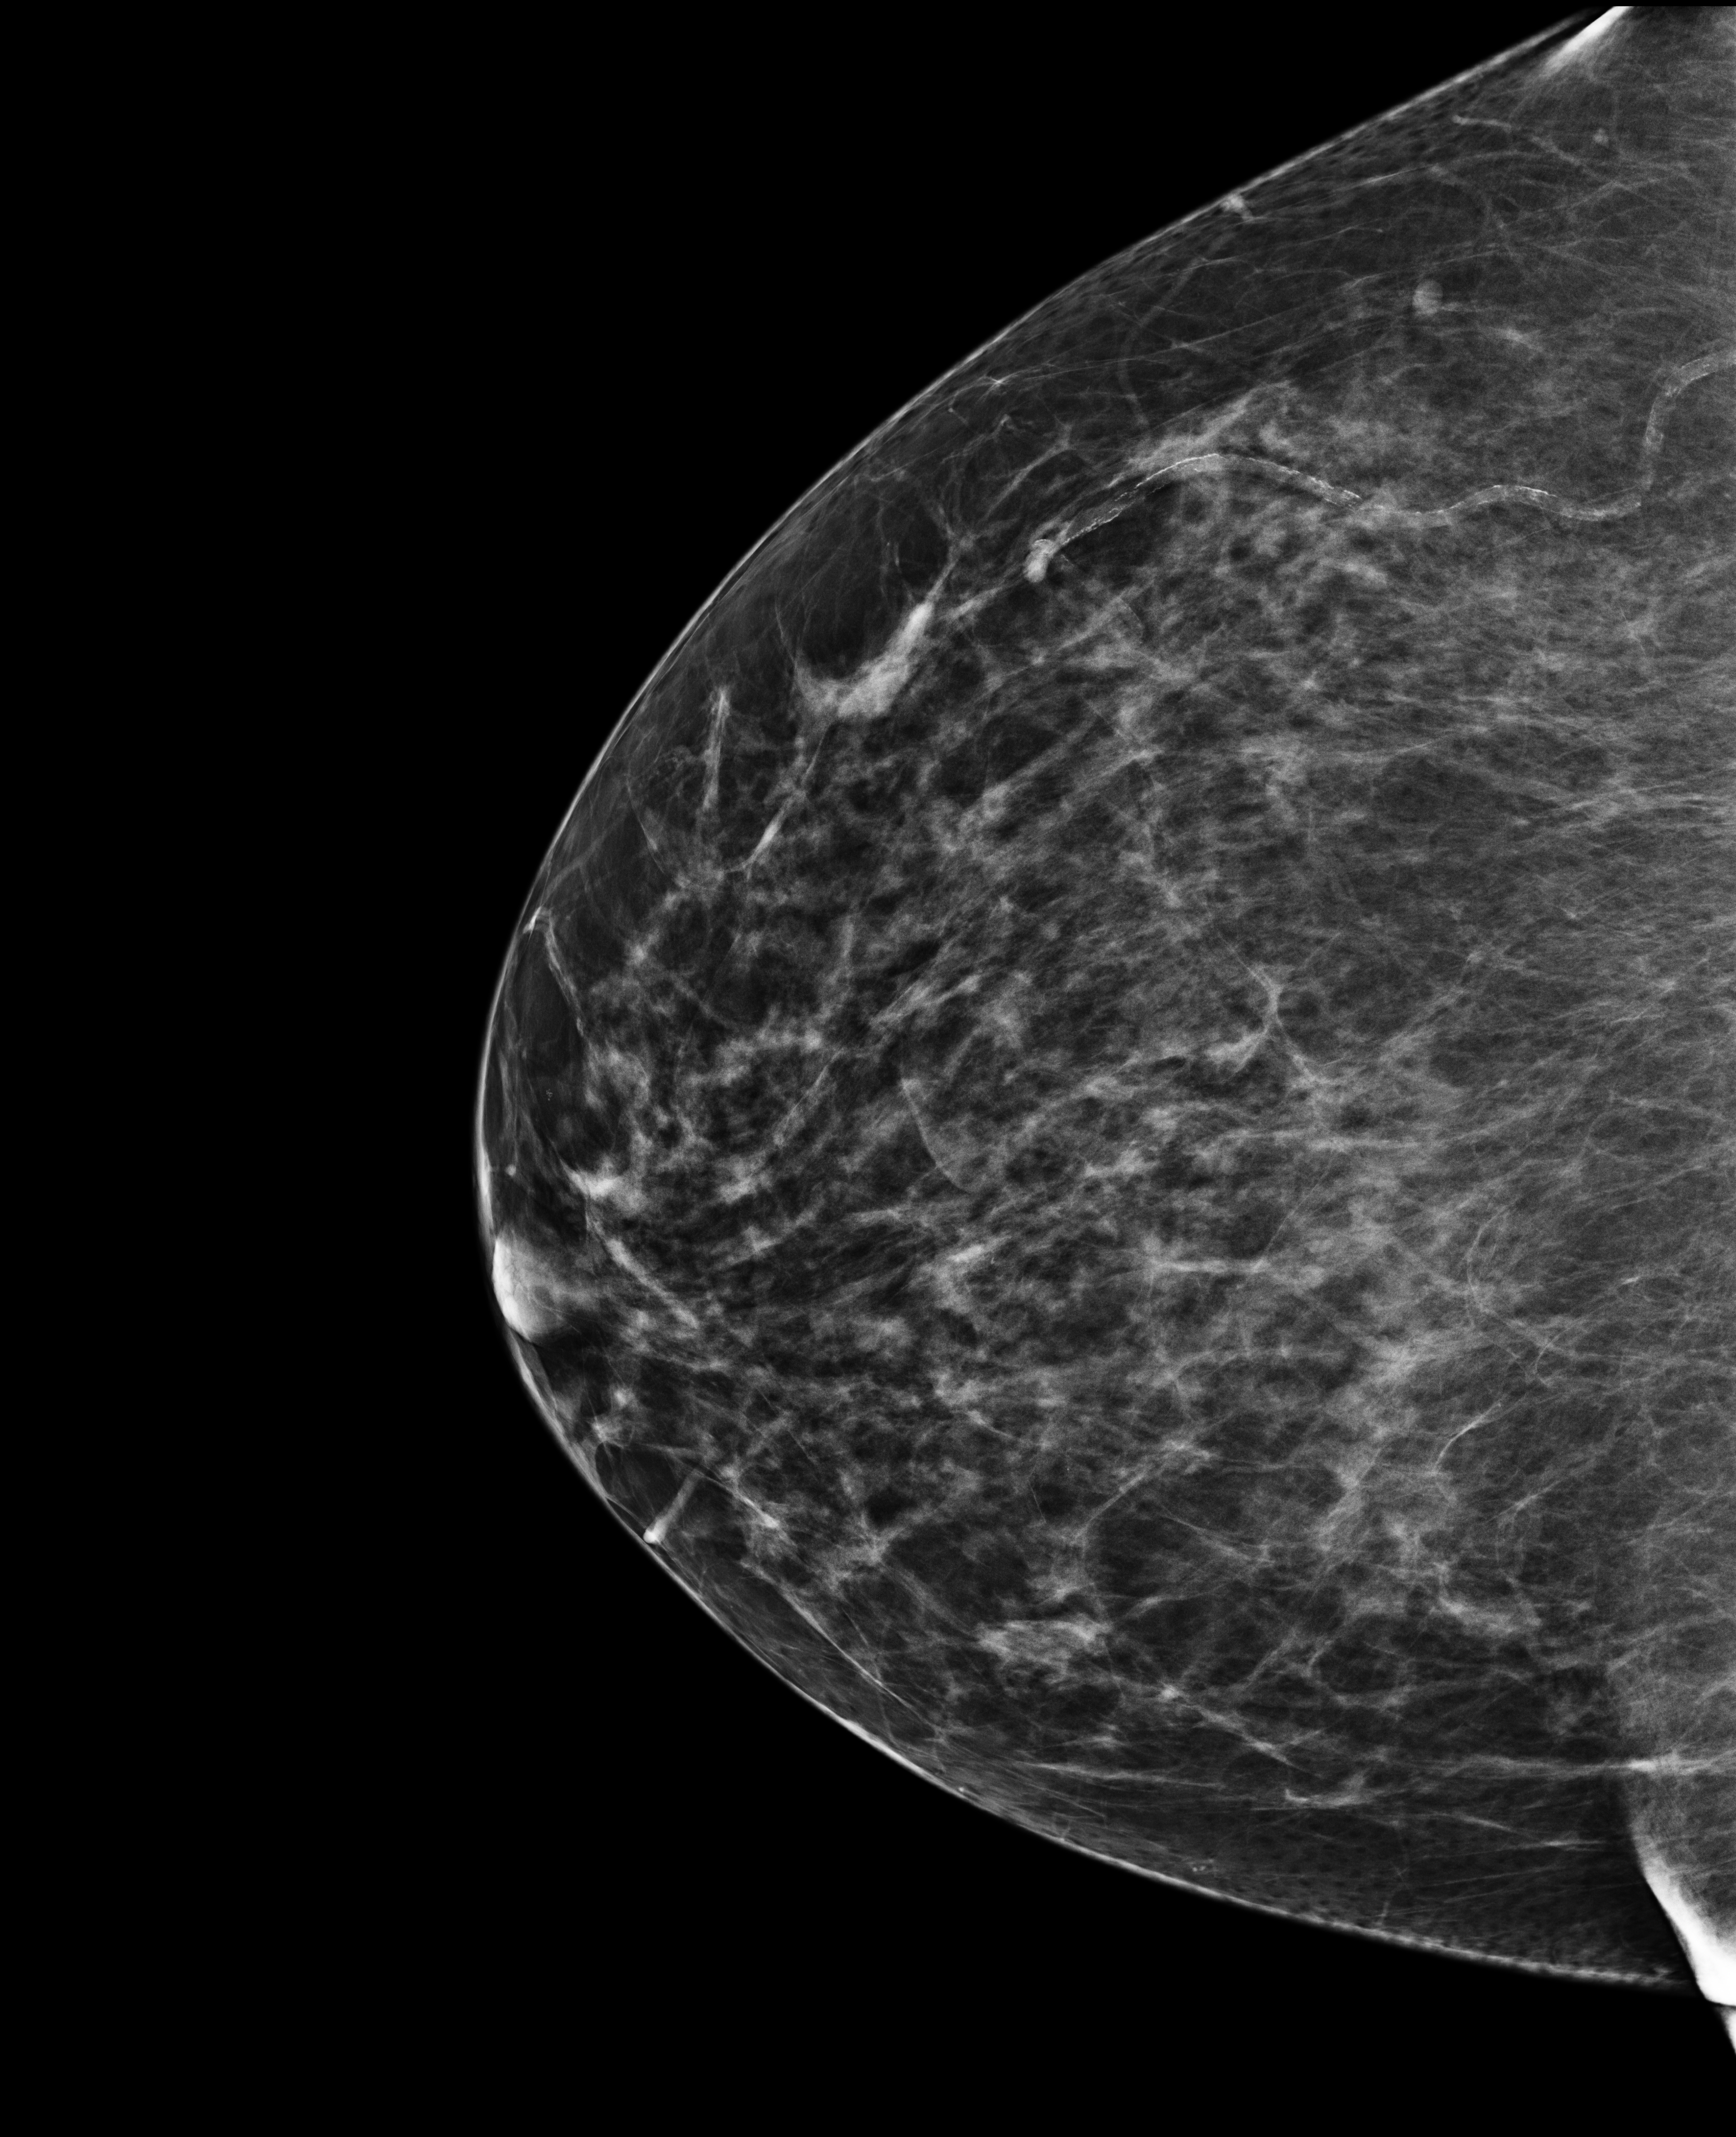
Screening examination, compressed breast thickness 82 mm, system: Selenia Dimensions. Patient: female, 68 years.
Image type: full-field digital mammogram. Breast: right. Projection: cranio-caudal projection.